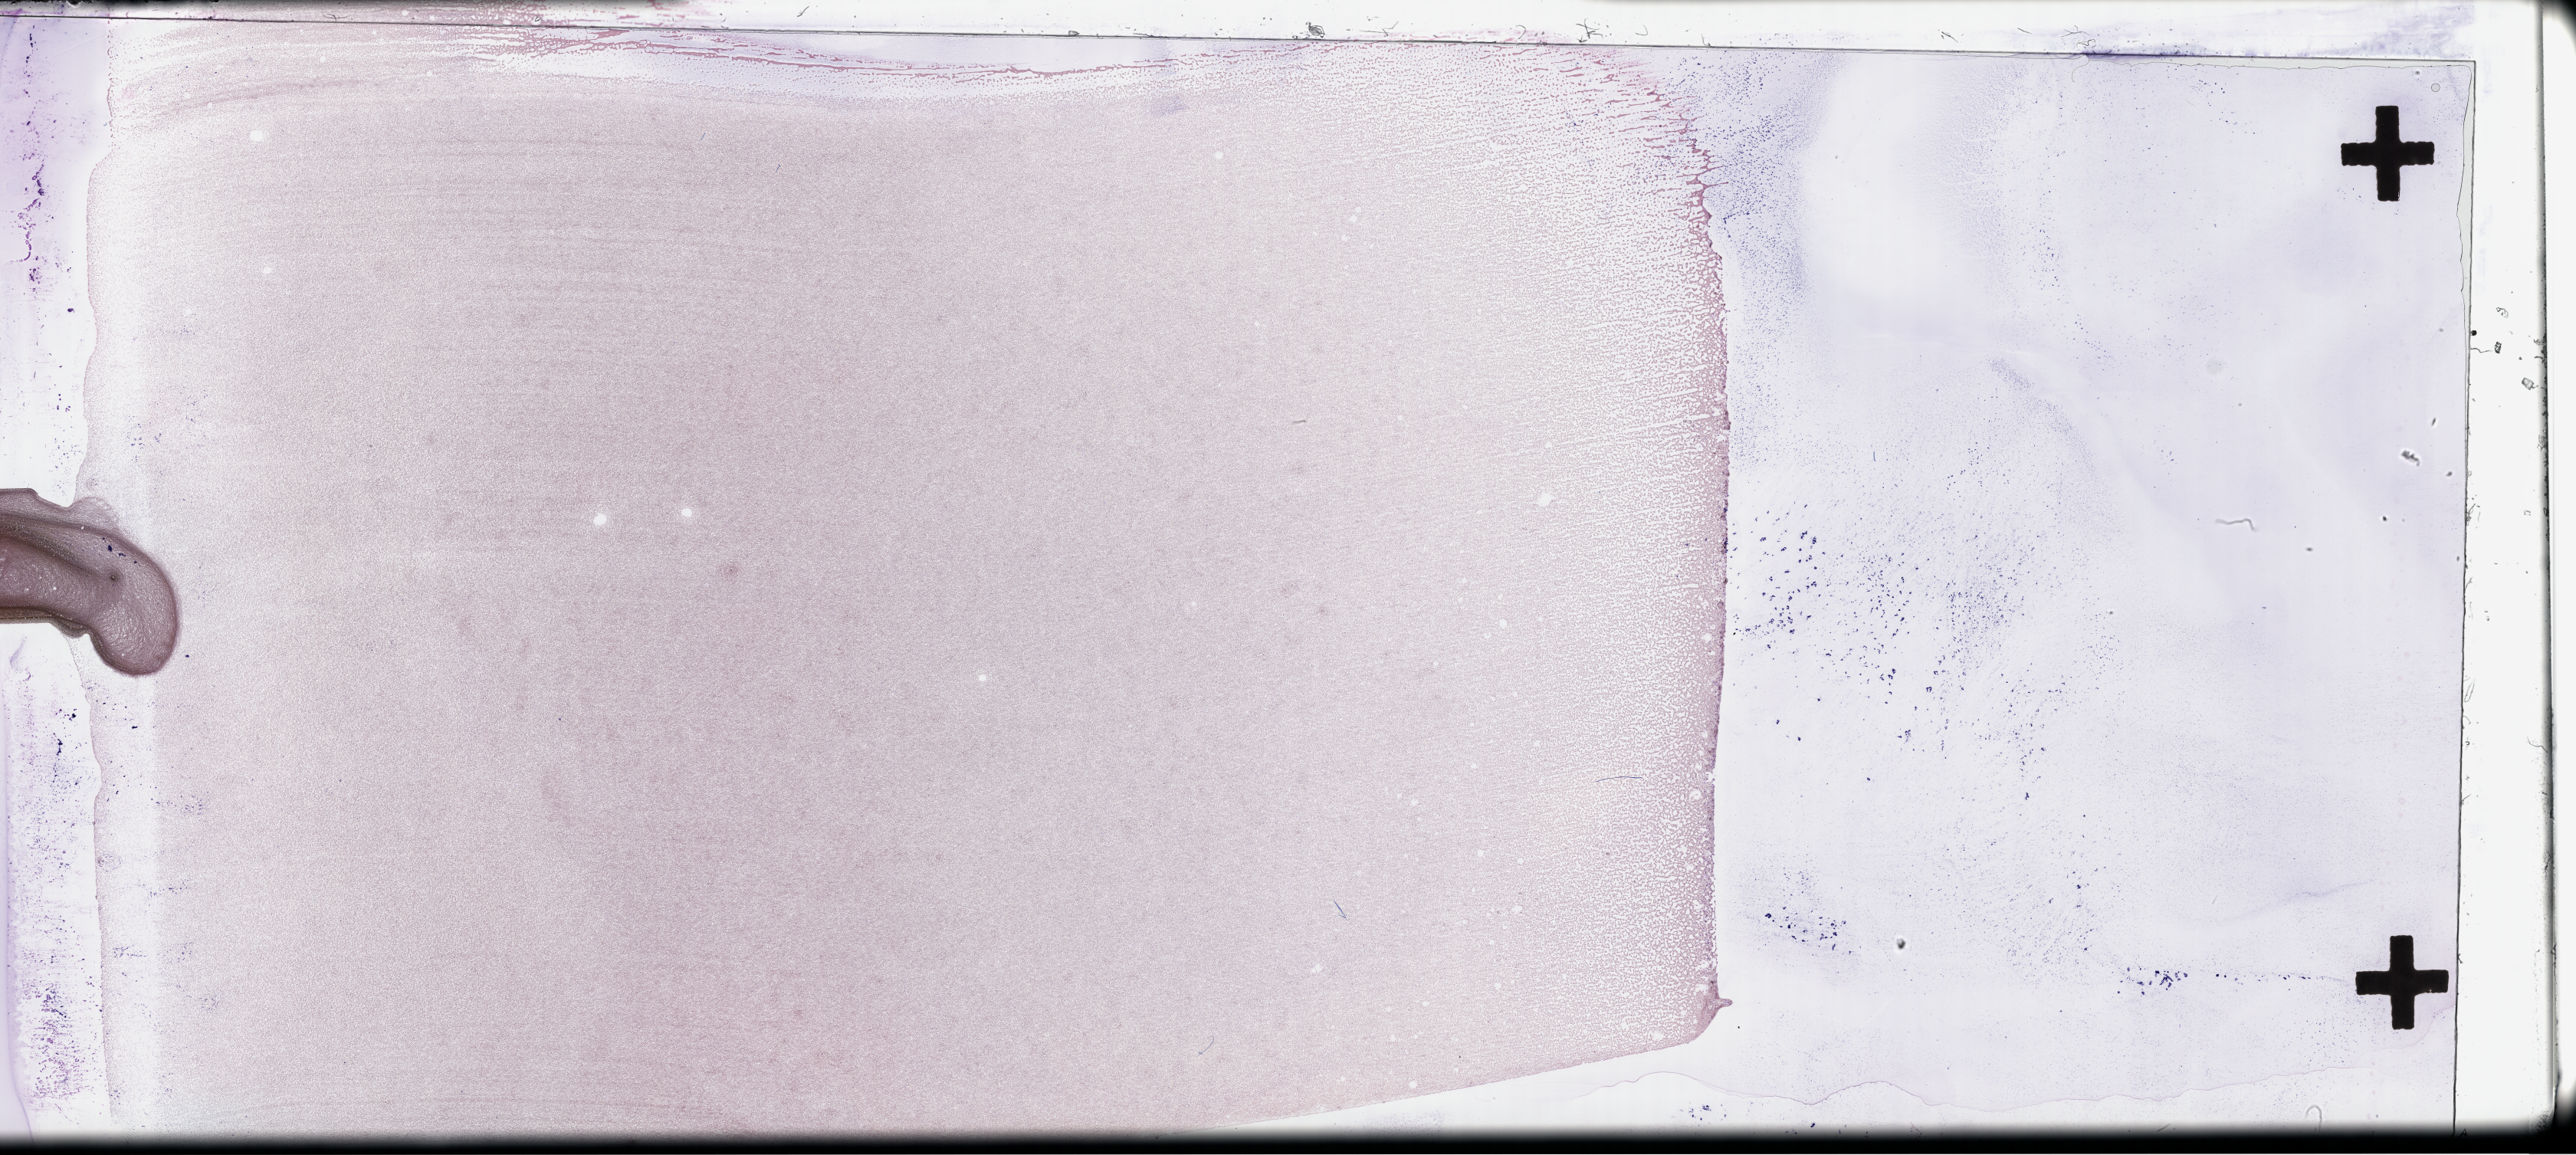
Wright-Giemsa-stained bone marrow smear, whole-slide image, low-resolution overview of the scanned area, about 54.3 x 24.3 mm; specimen time point: collected at disease progression. Female patient.
• from a patient with: Plasma Cell Myeloma